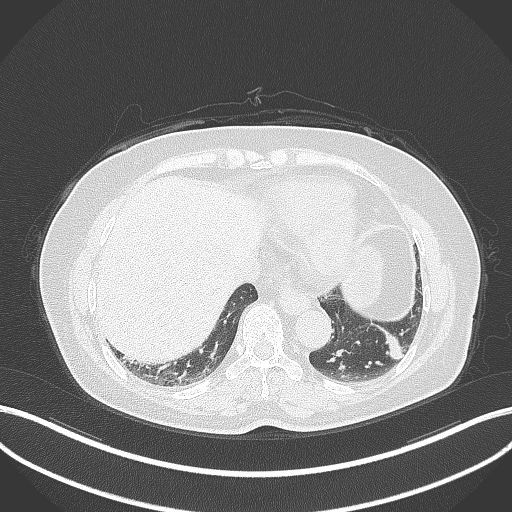
Chest CT, one axial slice. Slice 102 of 311 in the series (ordered by position). Reconstruction kernel B70f. 120 kVp. Lung window (W 1500 / L -600 HU). 1 mm slice thickness. 512 × 512 image matrix, field of view 400 × 400 mm. Female patient, age 59 years. From the clinical record (not read from this slice): clinical TNM (as recorded): T2a N0 M0.
Outlined on this slice (rectangle marked by the reading radiologist):
- lung tumour (recorded histology: adenocarcinoma): bounding box <372,319,407,365> (left, top, right, bottom; pixels)